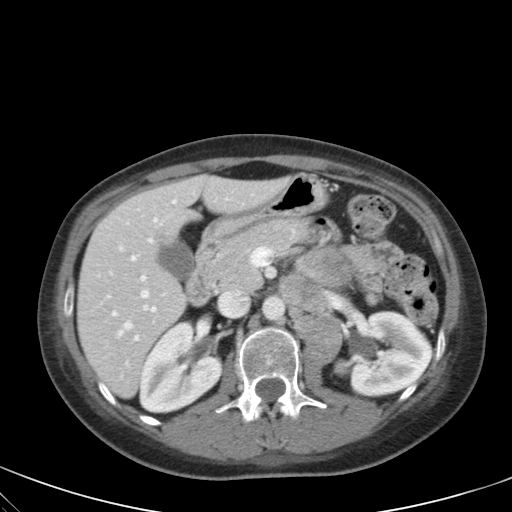
Contrast-enhanced abdominal CT, one axial slice. Slice 29 of 59 in the series (ordered by position). Soft-tissue window (W 400 / L 40 HU). 512 × 512 image matrix. Female patient, age 28 years. From the clinical record (not read from this slice): diagnosis: adrenocortical carcinoma; tumour side: left adrenal.
Annotated regions visible in this slice (semi-automatically segmented with operator editing):
- mass: bounding box [x1, y1, x2, y2] px = [300, 250, 347, 283]